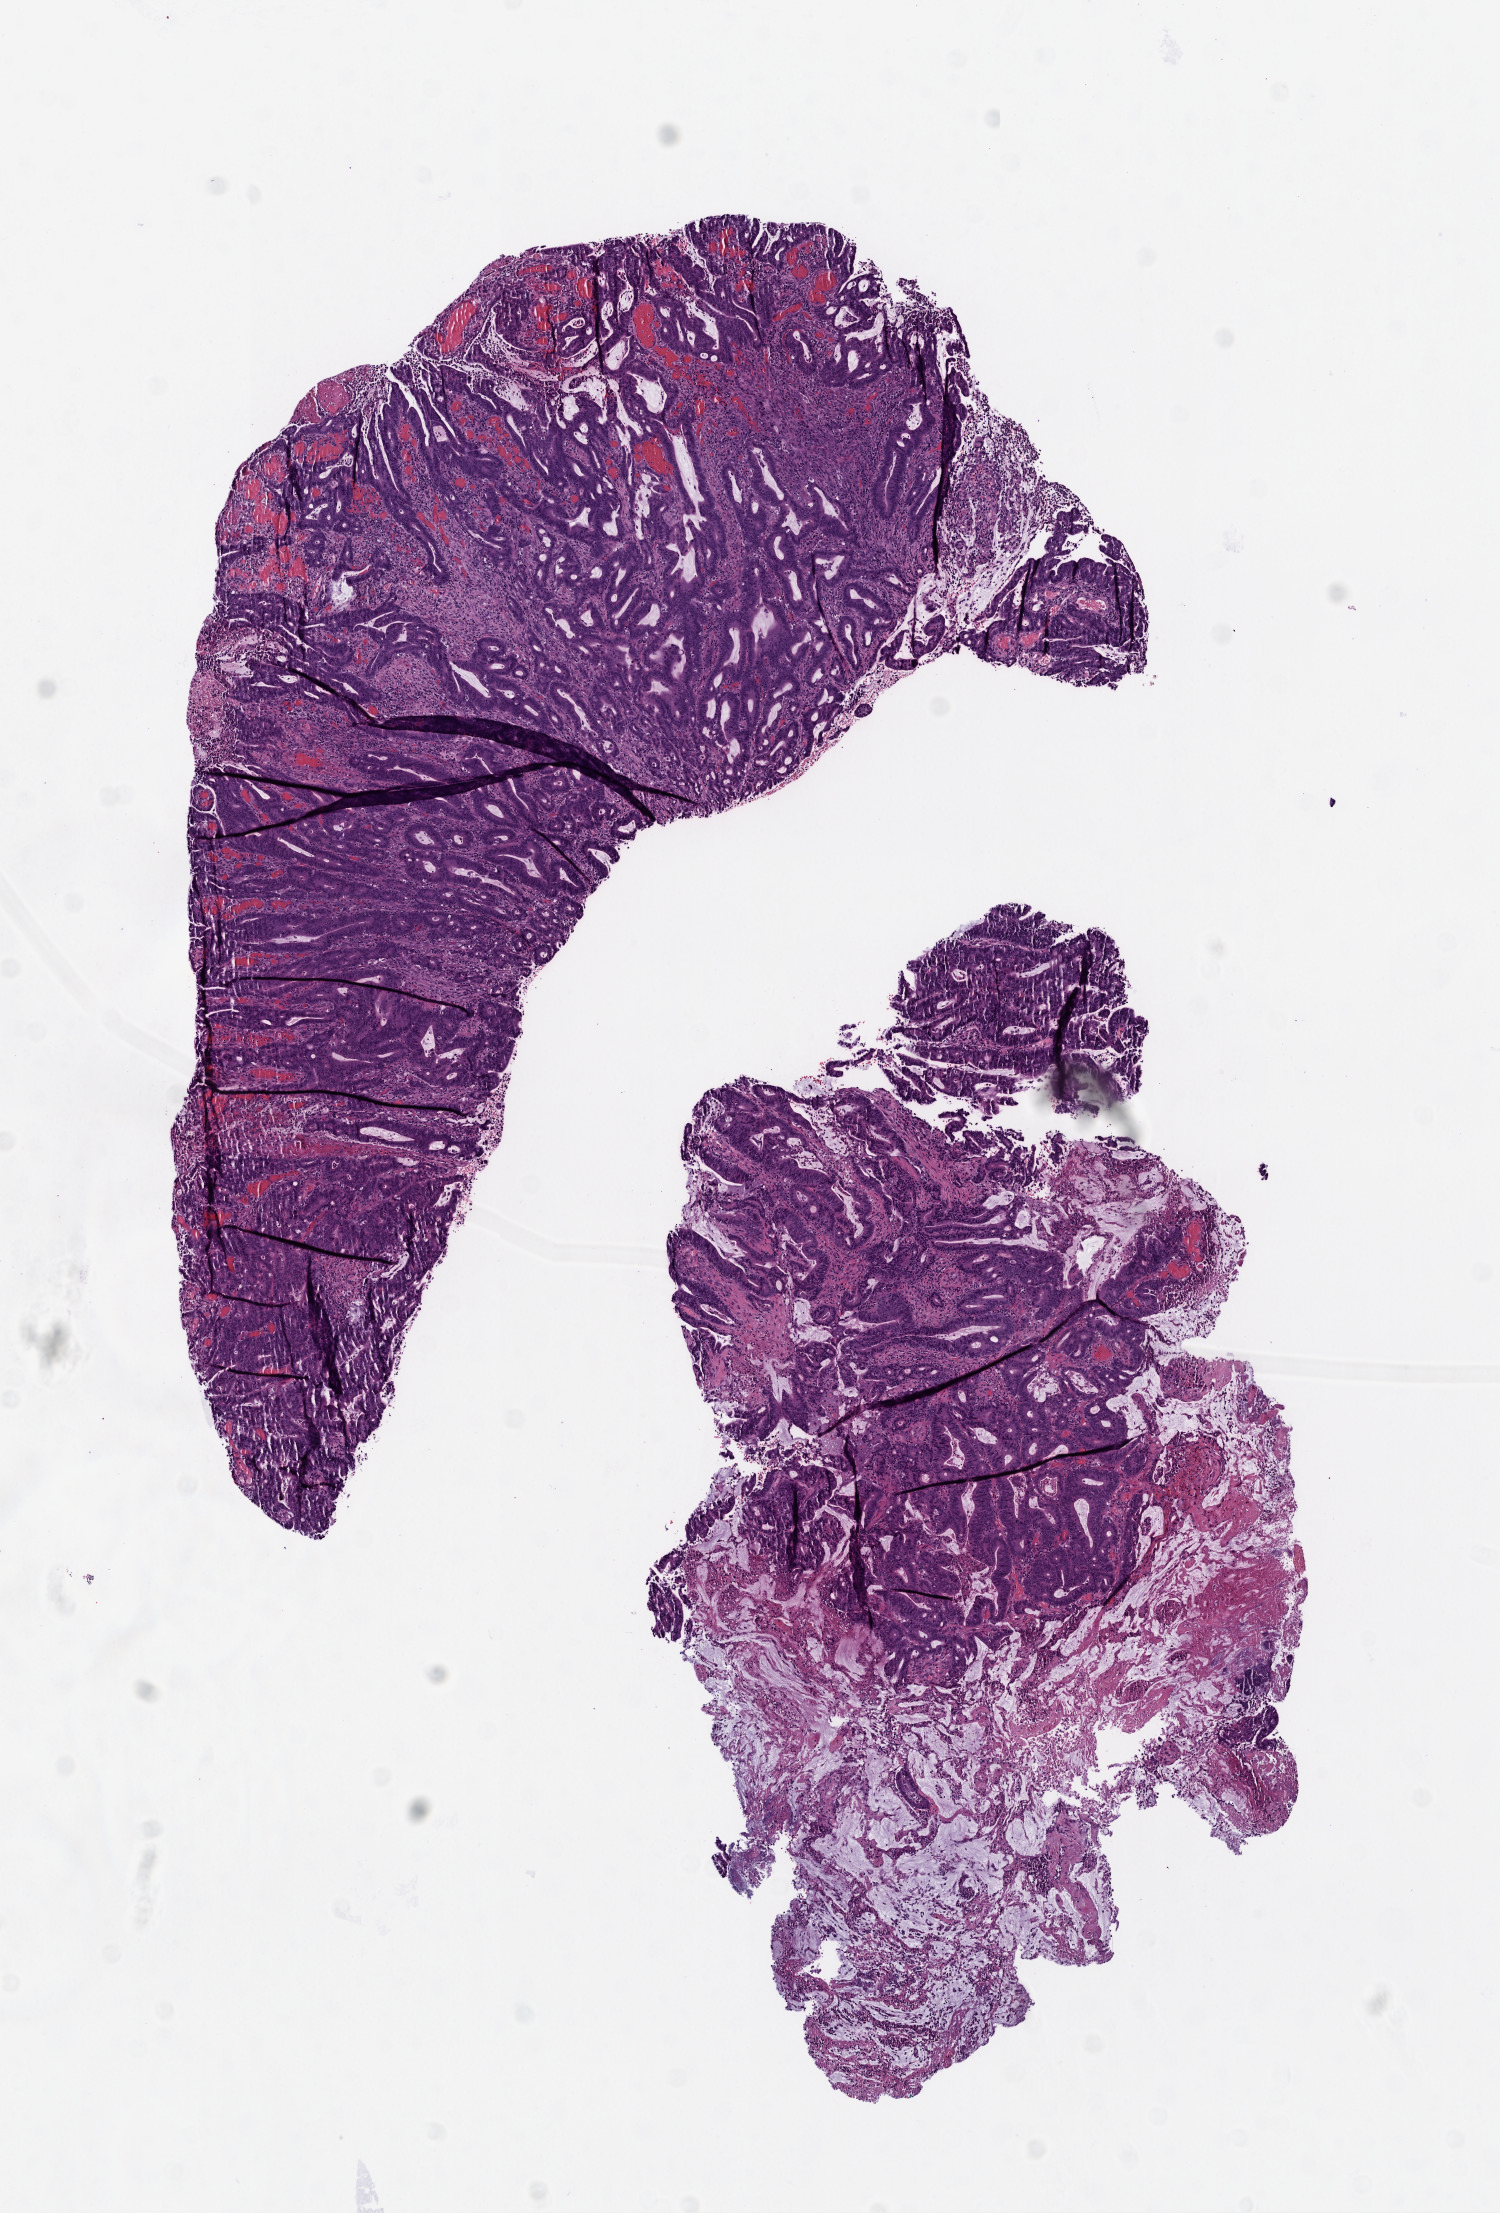
Whole-slide histology image, Hematoxylin and eosin (H&E) stained, a low-resolution overview of the entire scanned area, about 6.0 x 8.9 mm (acquisition: 20x scan). Frozen section. Colon, primary tumour sample. Female, age 71 years at initial diagnosis. Pathologist review of this section (percent, as recorded): tumour cells 89%, tumour nuclei 80%, normal cells 0%, stromal cells 10%, necrosis 1%.
• AJCC pathologic stage: IIB
• histologic diagnosis: Mucinous adenocarcinoma